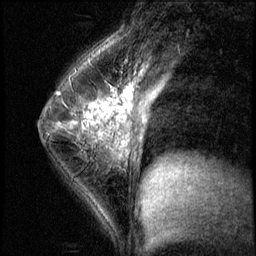
Breast MRI (dynamic contrast-enhanced), one sagittal slice; position 36 of 56 along the scan axis; 3 images stored at this slice position (order not interpretable as contrast timing); 1.5 T; TE 4.2 ms, TR 8.7 ms; 2.5 mm slice thickness; 256 × 256 image matrix, field of view 180 × 180 mm. Patient: female, 35 years. From the clinical record (not read from this slice): setting: breast cancer imaged before/during neoadjuvant chemotherapy; receptor status: HER2-positive.
Annotated regions visible in this slice (semi-automatically segmented with operator editing):
- analysis volume of interest (the breast-tissue region the enhancement analysis was run in; not a lesion): bounding box (x1, y1, x2, y2) in pixels: (58, 84, 138, 186)
- tumour enhancement mask (voxels above the 140 % enhancement threshold inside the analysis volume of interest): (58, 93, 102, 137)